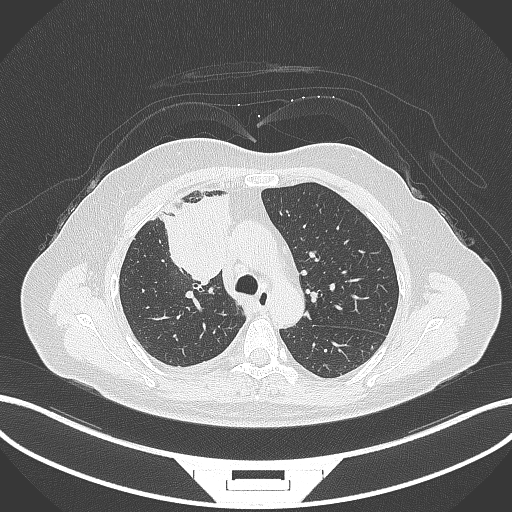
Chest CT, one axial slice. Position 200 of 305 along the scan axis. Lung window (W 1500 / L -600 HU). 1 mm slice thickness. 512 × 512 image matrix, field of view 400 × 400 mm. Patient: female, 52 years. From the clinical record (not read from this slice): clinical TNM (as recorded): T3 N1 M1.
Structures marked on this image (bounding box drawn by a radiologist):
- lung tumour (recorded histology: adenocarcinoma): bounding box (x1, y1, x2, y2) in pixels: (158, 192, 232, 284)